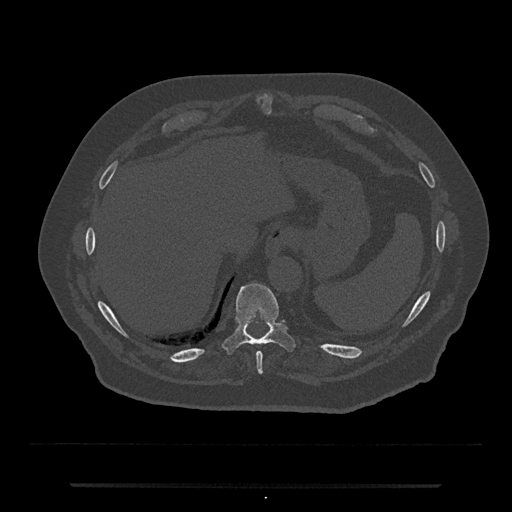
CT including the spine, one axial slice. Position 714 of 797 along the scan axis. Reconstruction kernel Br40s/3. 120 kVp. Bone window (W 1800 / L 400 HU). 0.5 mm slice thickness. 512 × 512 image matrix, field of view 434 × 434 mm. Patient: male, 80 years. Case-level facts recorded for this patient, not image findings: primary cancer: prostate.
Structures marked on this image (semi-automatically segmented with operator editing):
- T10 vertebra: box from (x=223, y=283) to (x=295, y=354) px
- T9 vertebra: (x=256, y=352)–(x=263, y=374)